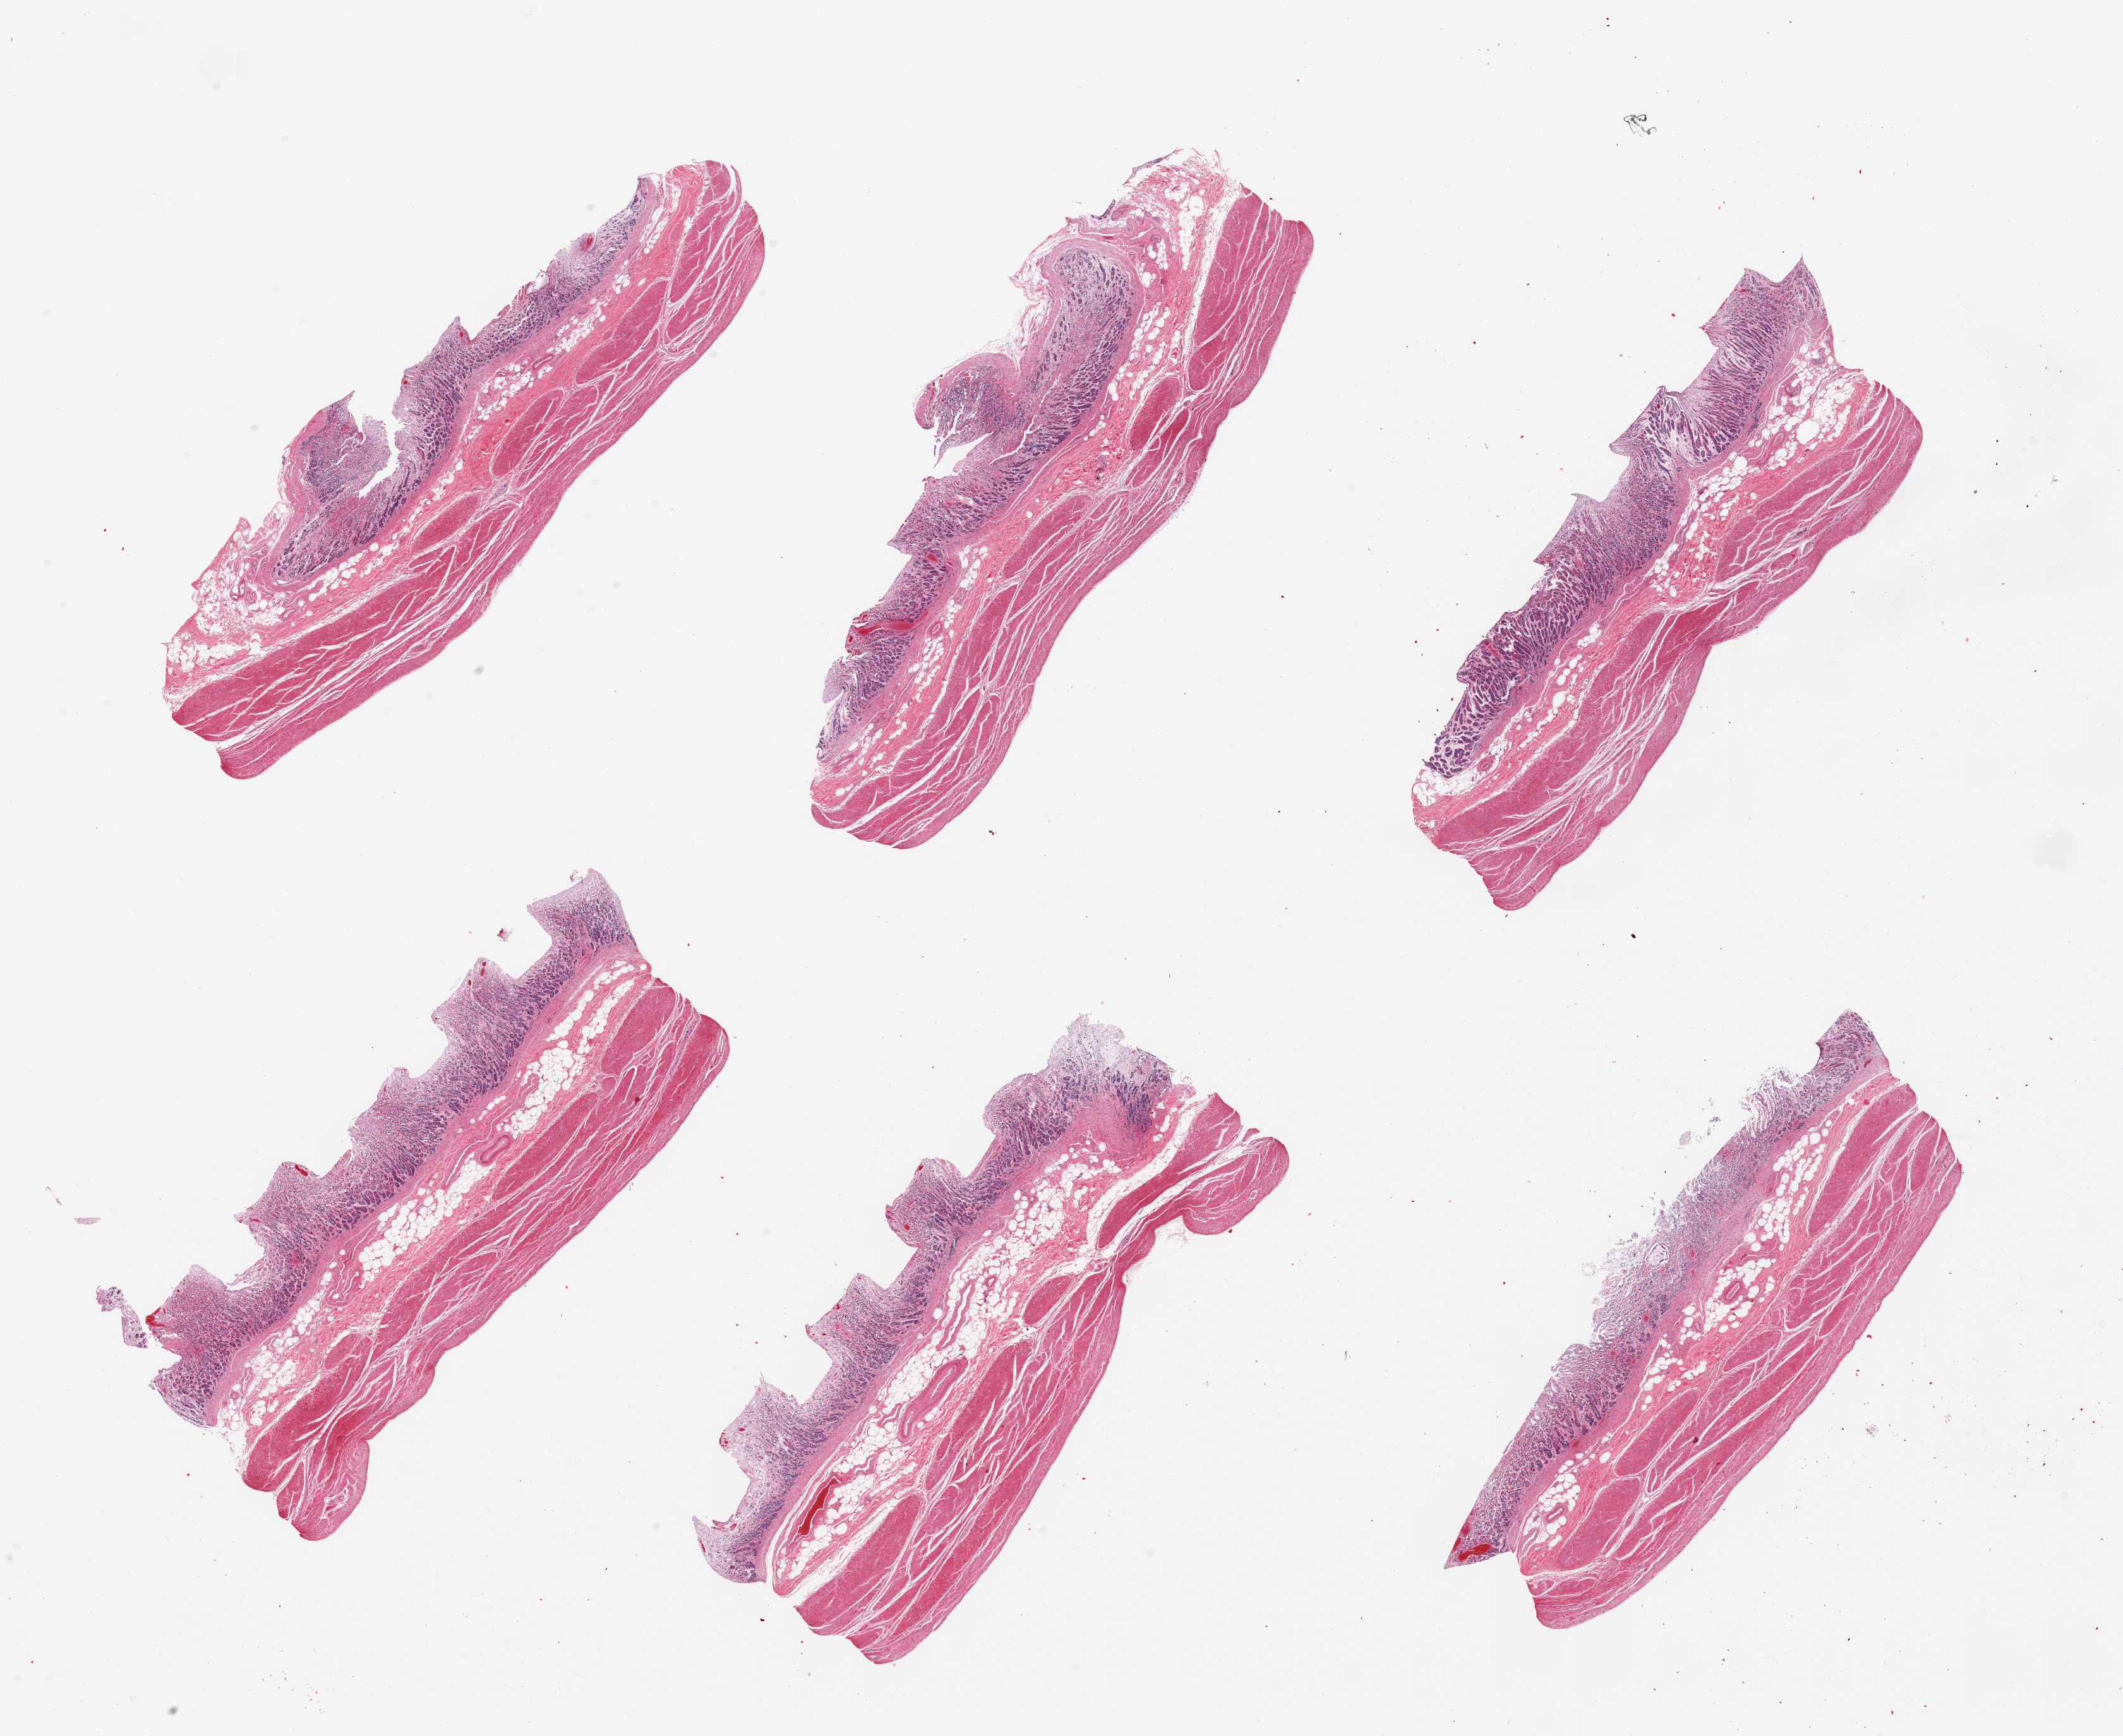
Whole-slide image, H&E stain — a low-resolution overview of the entire scanned area, about 26.6 x 21.7 mm (acquisition: 20x scan). PAXgene-fixed, paraffin-embedded tissue. Target tissue: stomach. Donor tissue sample. Donor: male.
Reviewer comment on this tissue sample: 6 pieces, muscularis and moderately autolyzed mucosa.